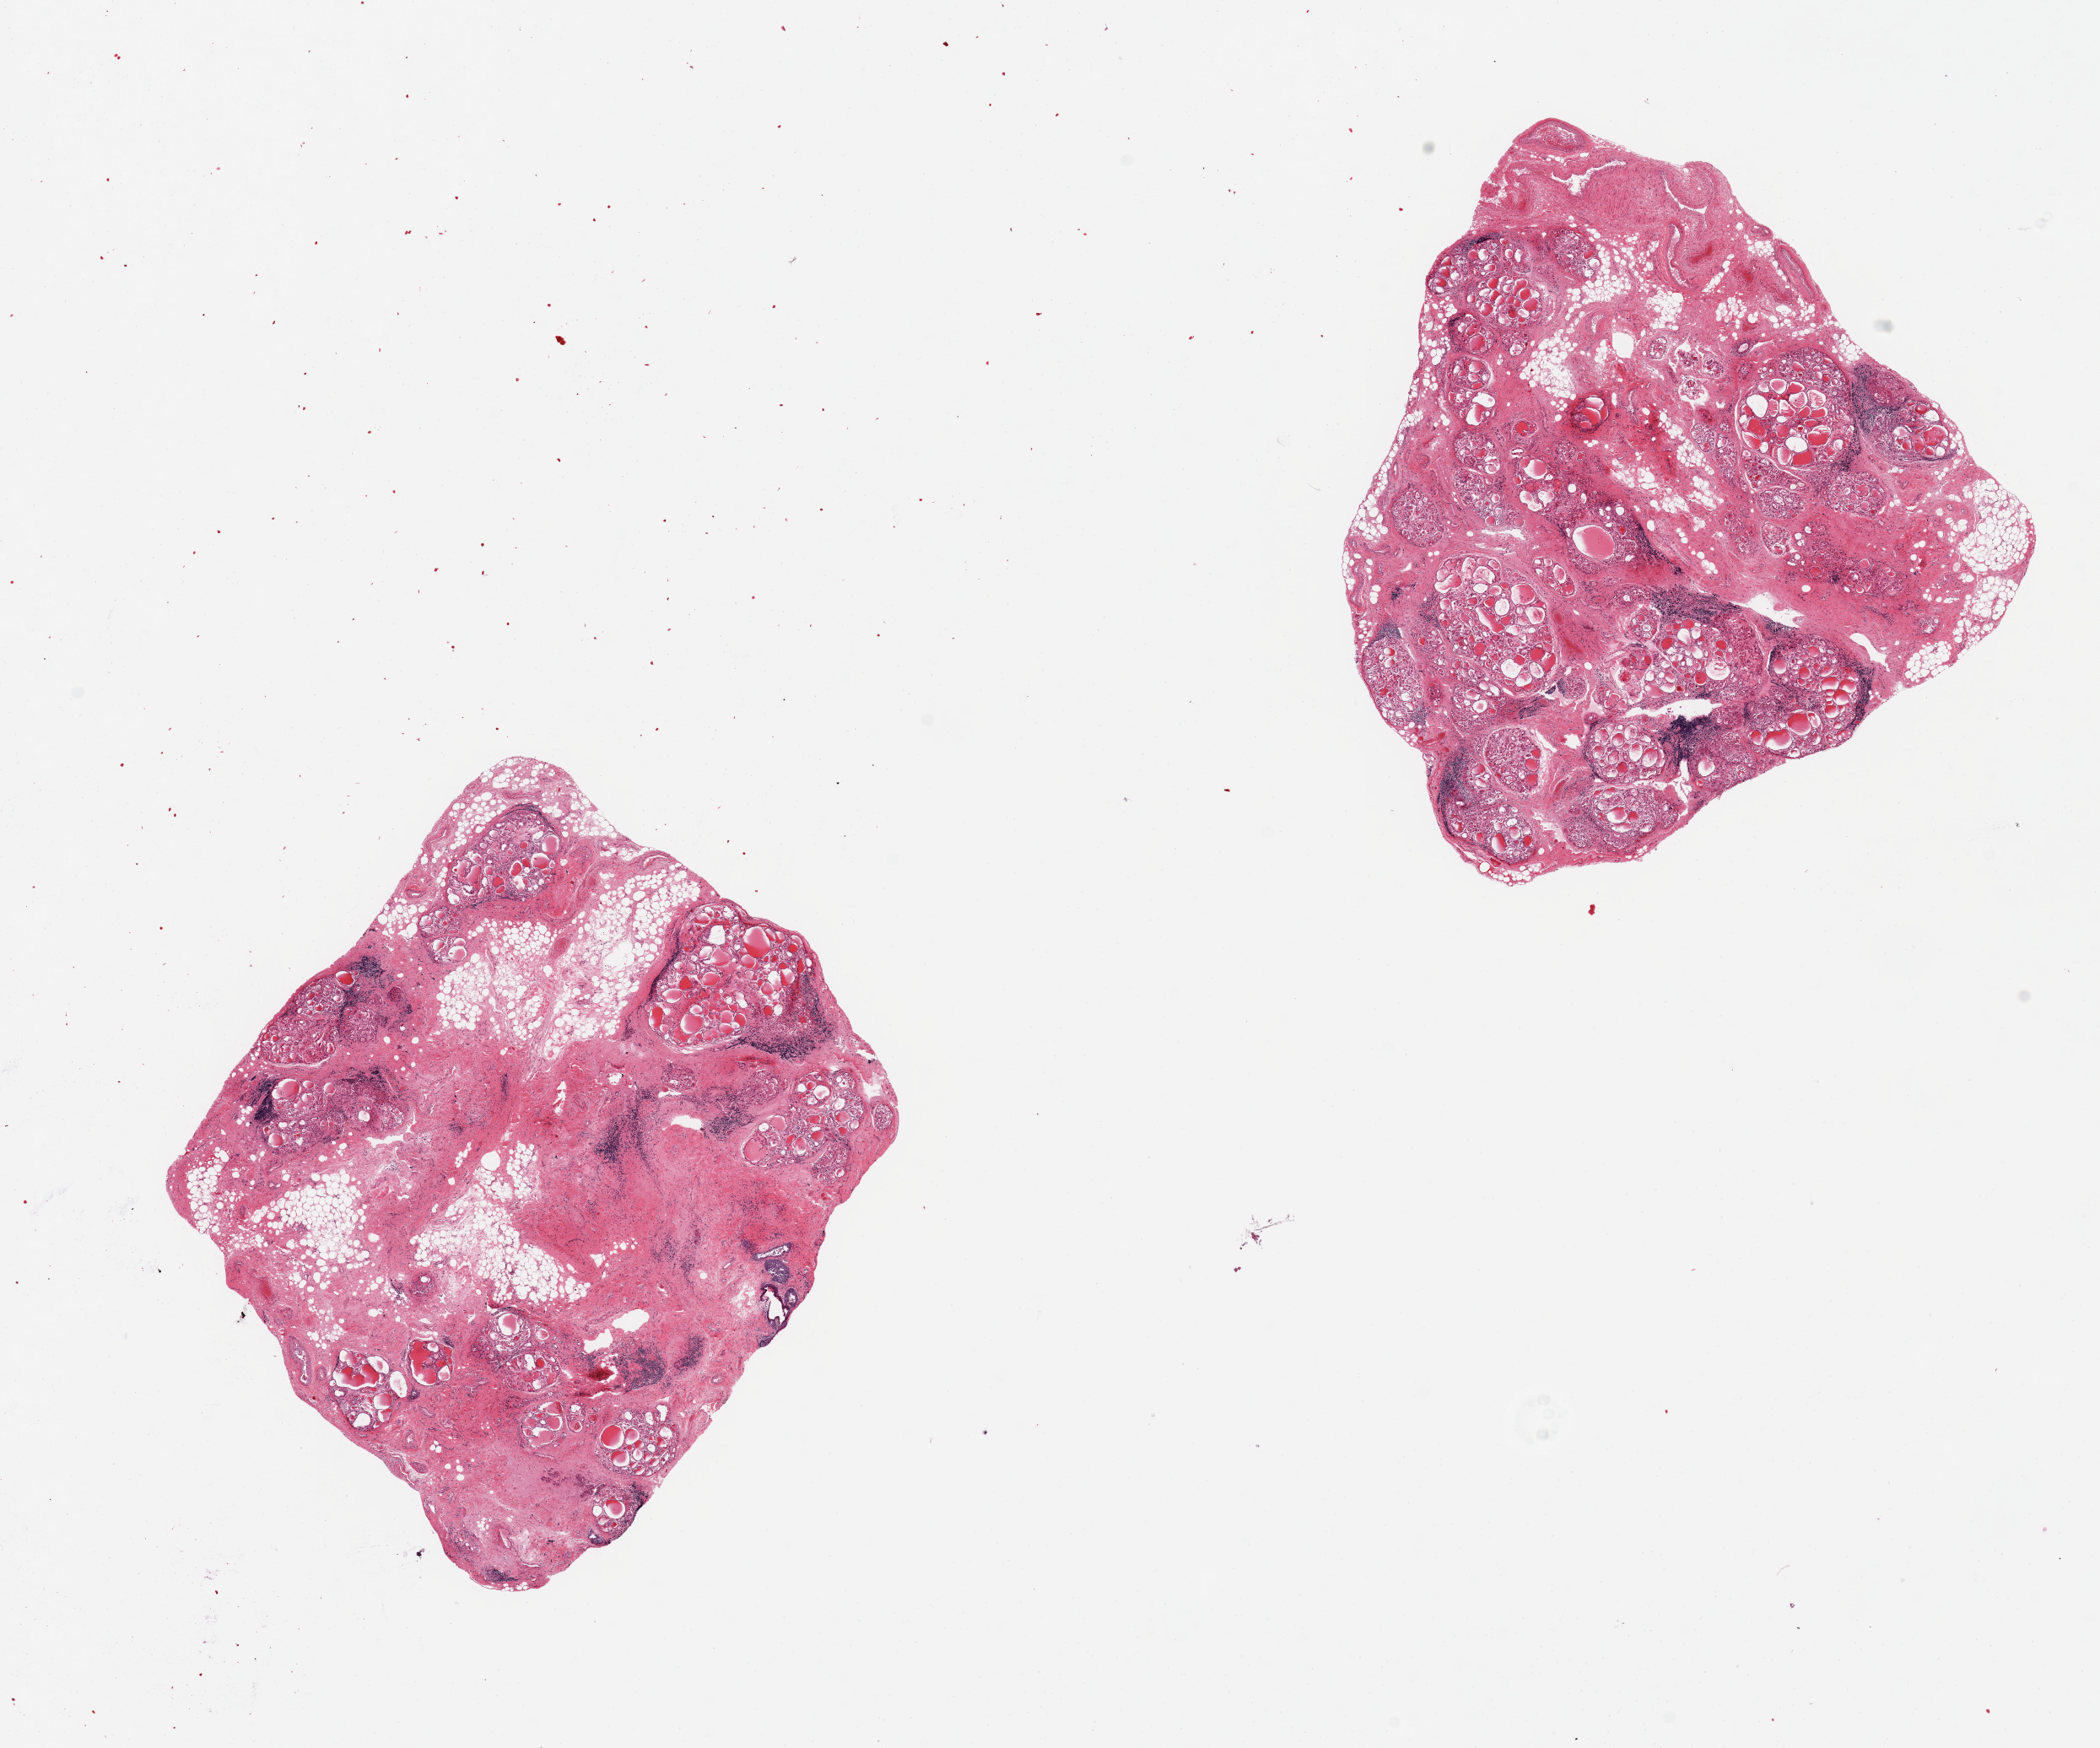
Haematoxylin and eosin whole-slide image, shown as a low-resolution overview of the whole scanned area (about 19.7 x 16.4 mm, slide scanned at 20x), PAXgene-fixed paraffin-embedded (PFPE) section, section of thyroid (target tissue), donor tissue sample. Female donor.
- review note (as recorded): 2 pieces, end-stage Hashimoto thyroiditis, marked regressive changes, mulitple foci adherent fat, several